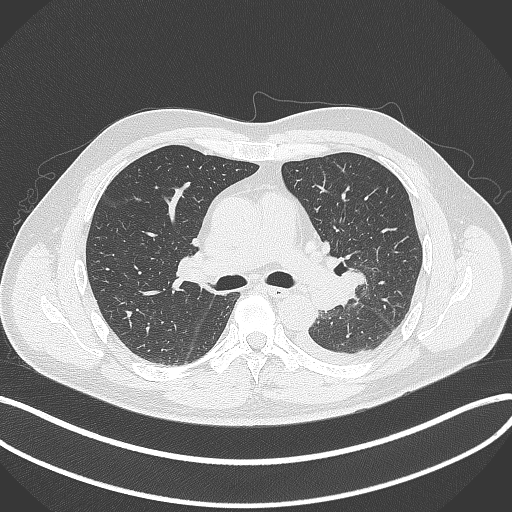
Chest CT, one axial slice. Position 220 of 342 along the scan axis. 120 kVp. Lung window (W 1500 / L -600 HU). 512 × 512 image matrix. Patient: male, 58 years. Case-level facts recorded for this patient, not image findings: clinical TNM (as recorded): T3 N1 M1b; histopathological grade: G3.
Structures marked on this image (bounding box drawn by a radiologist):
- lung tumour (recorded histology: small cell carcinoma): bounding box [x1, y1, x2, y2] px = [337, 265, 370, 293]